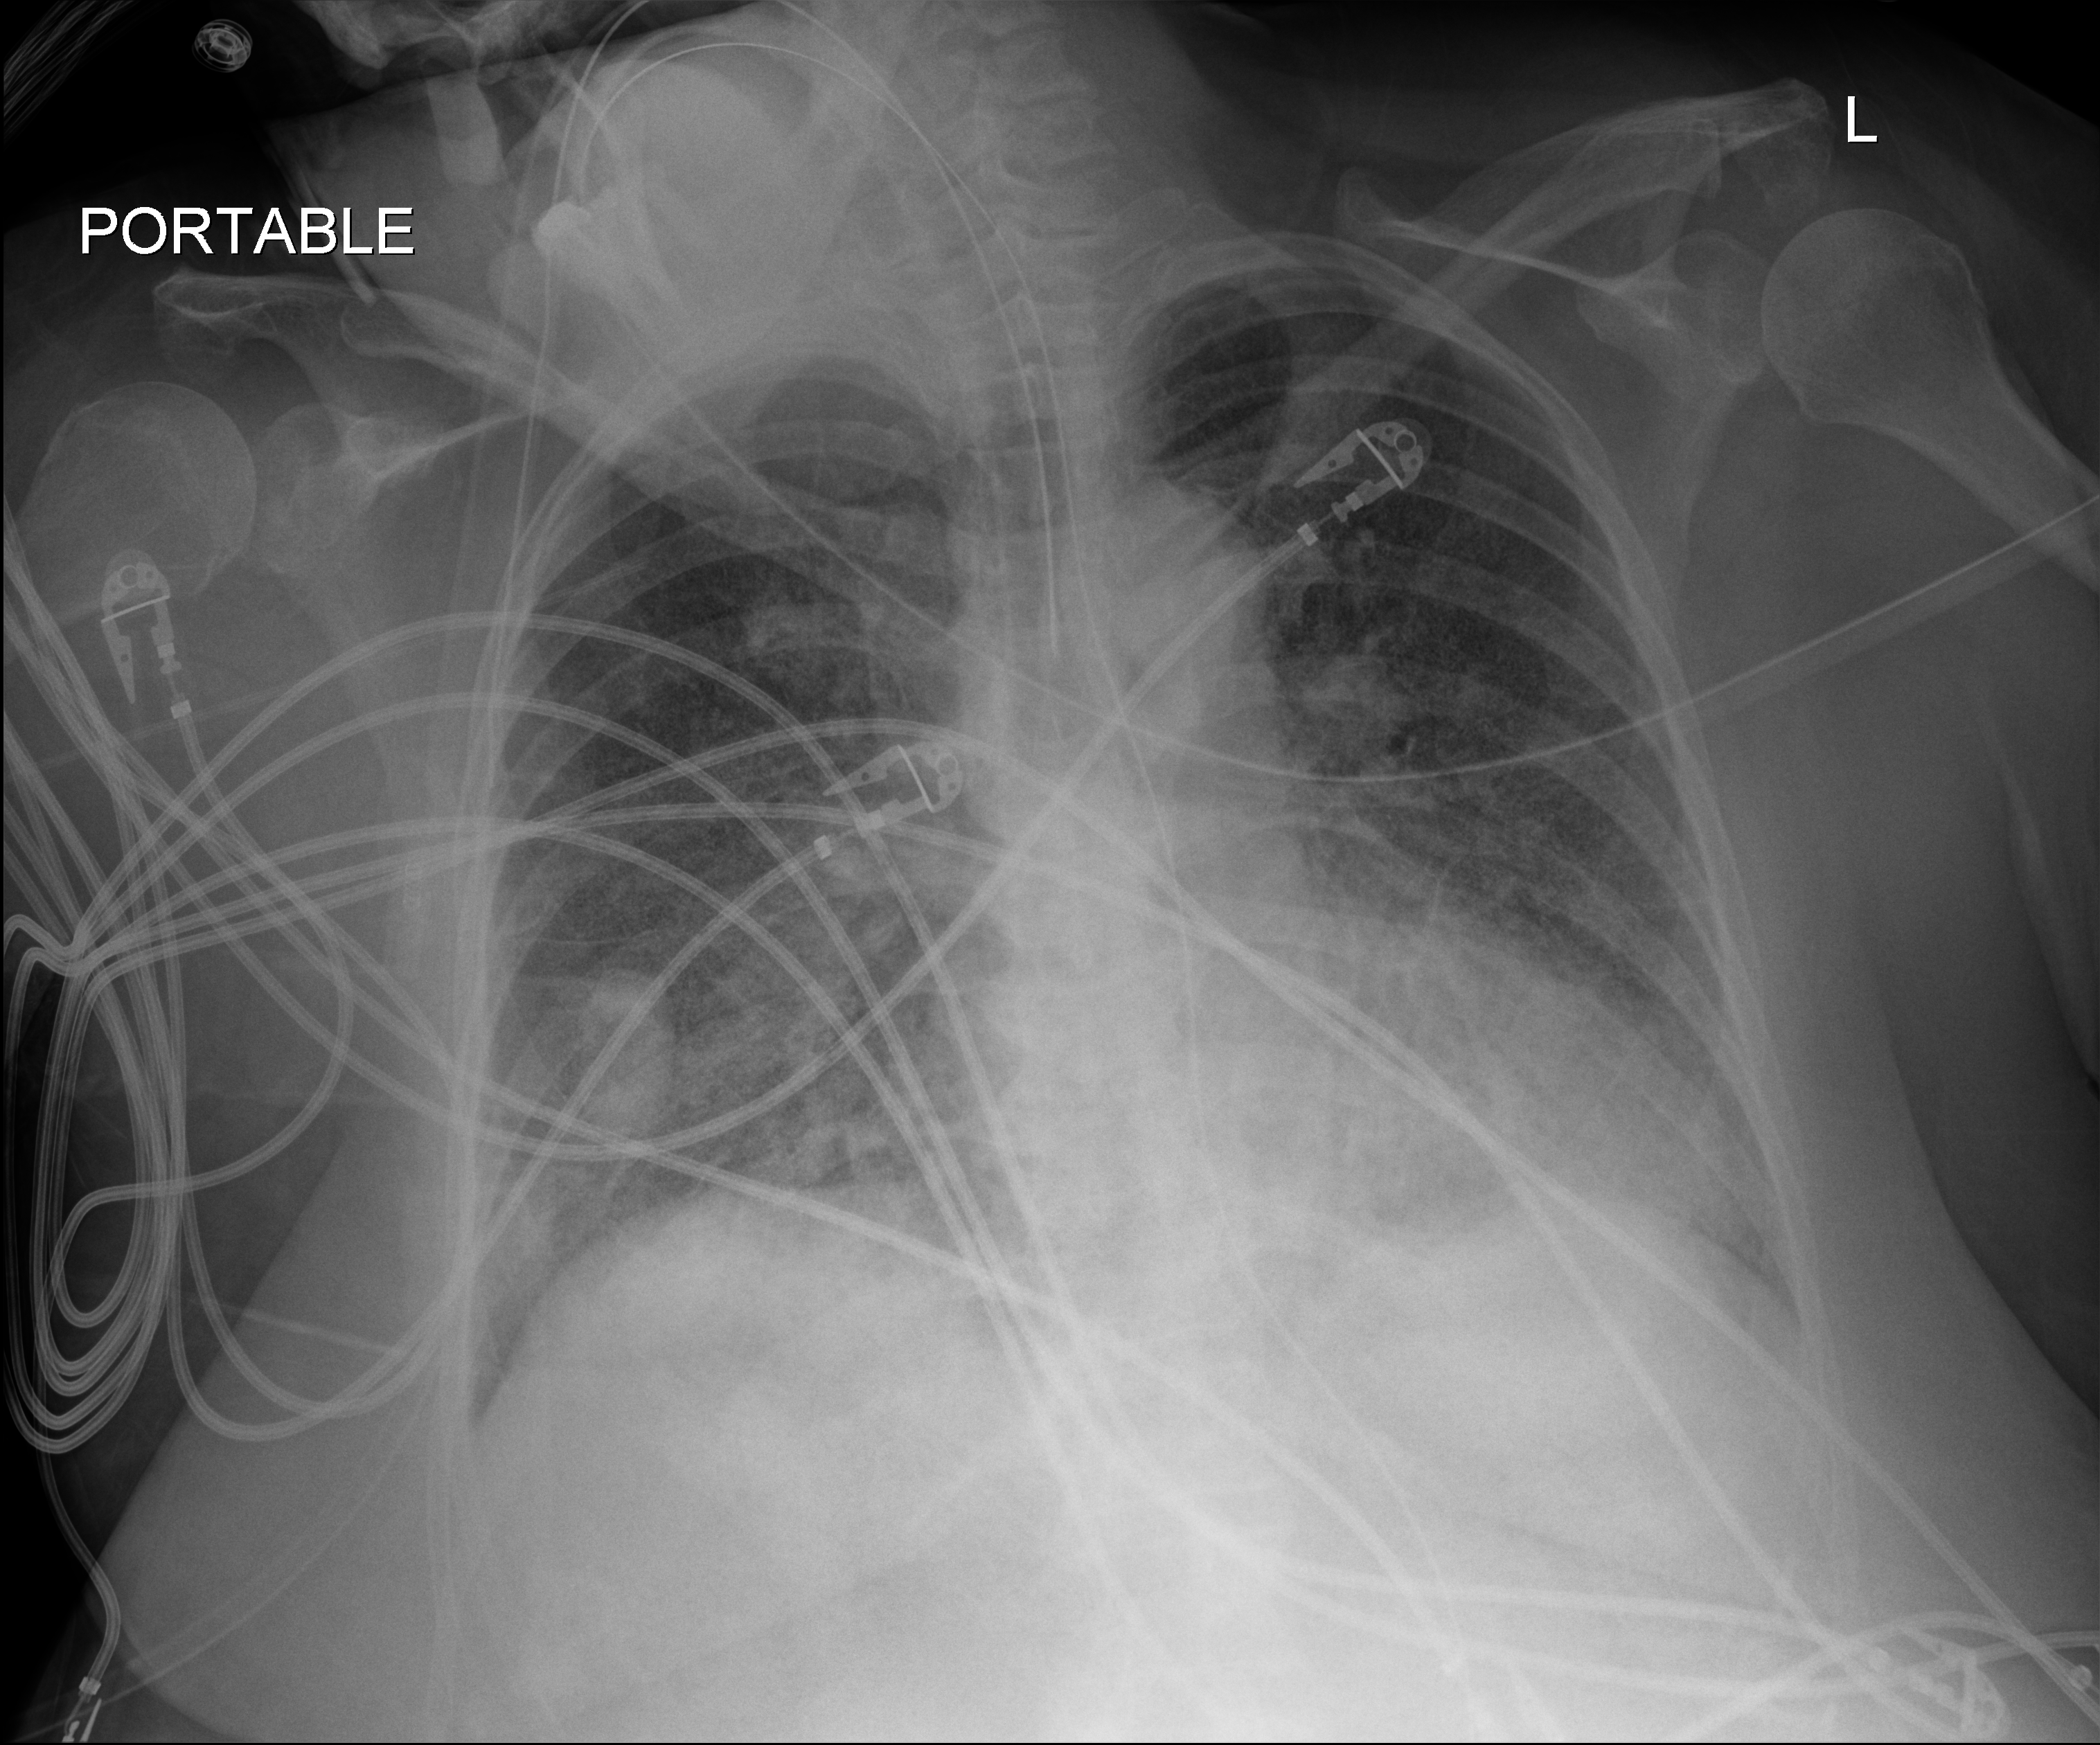
Chest radiograph. Patient hospitalised with COVID-19; female, aged 60–74 years.
From the hospital-stay record, not from the radiograph (when in the stay this image was taken is not recorded):
- mechanically ventilated during this hospital stay: yes
- hypertension (admission record): no
- diabetes (admission record): no